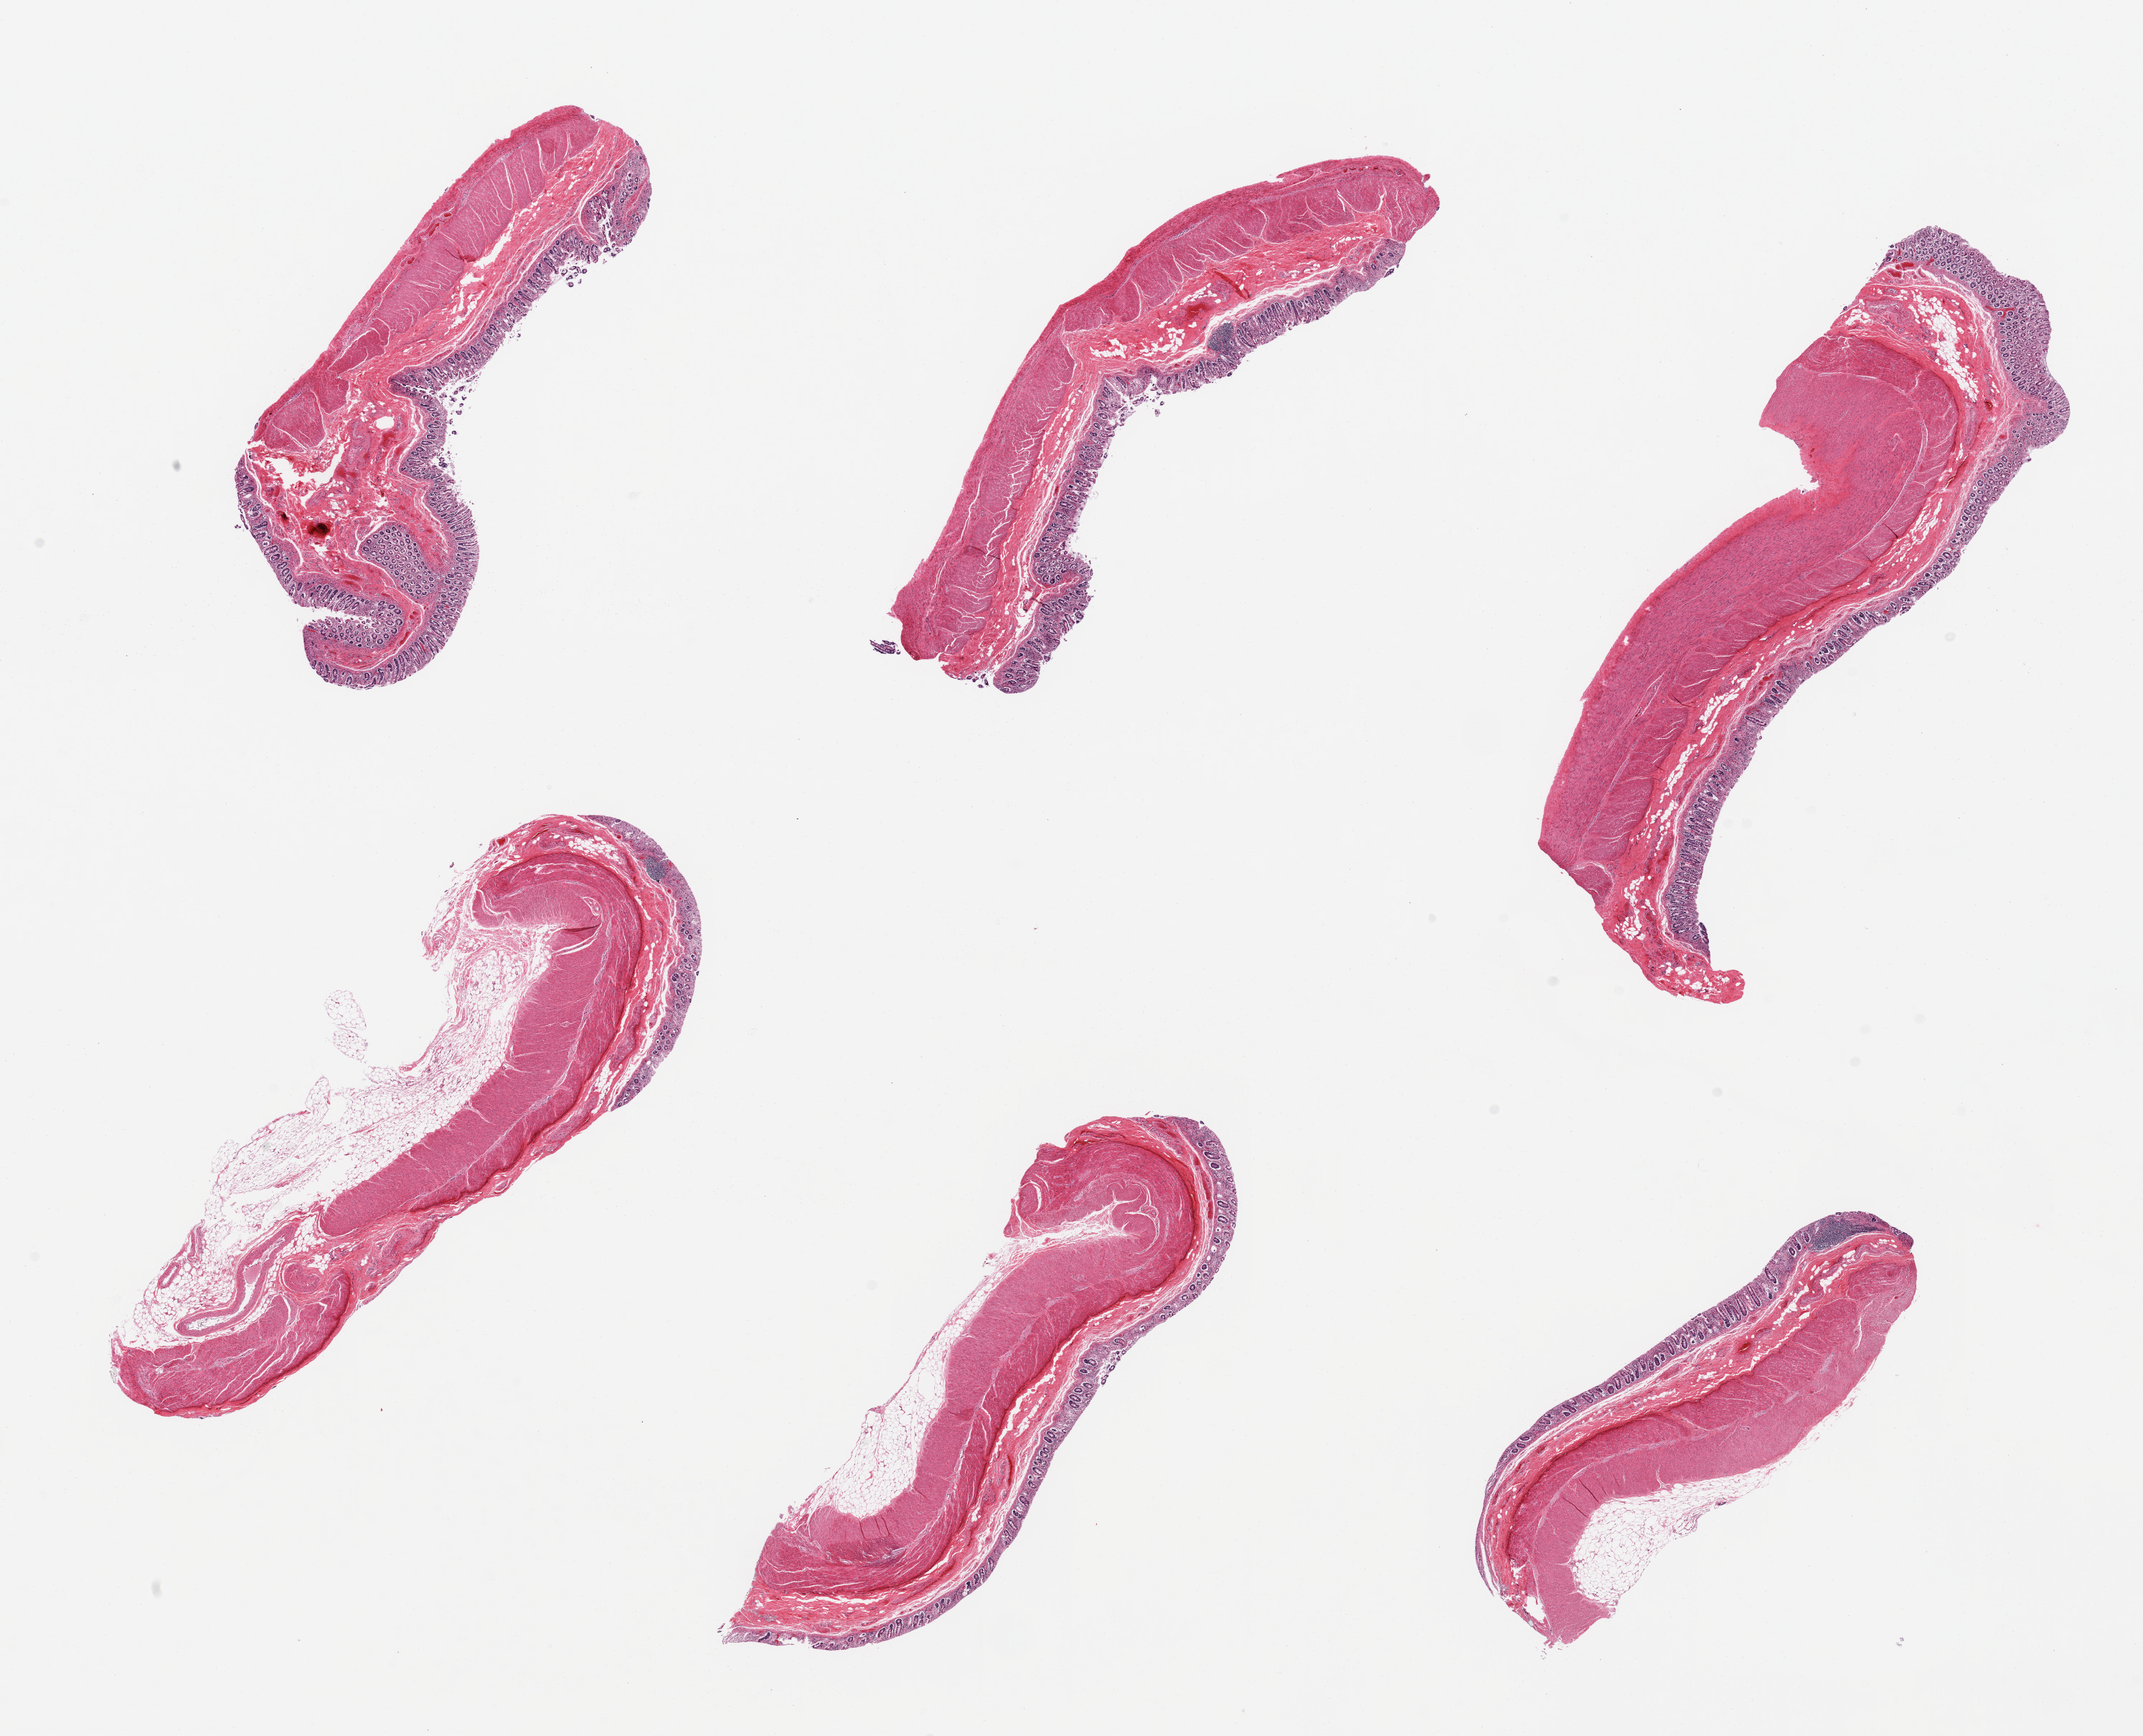
Whole-slide image, haematoxylin and eosin stain, whole scanned area (about 23.6 x 19.1 mm) shown as a low-resolution overview. PAXgene-fixed paraffin-embedded (PFPE) section. Section of transverse colon (target tissue). Tissue donor sample.
Reviewer comment on this tissue sample: 6 pieces, mucosa is badly autolyzed, ~20% of thickness.